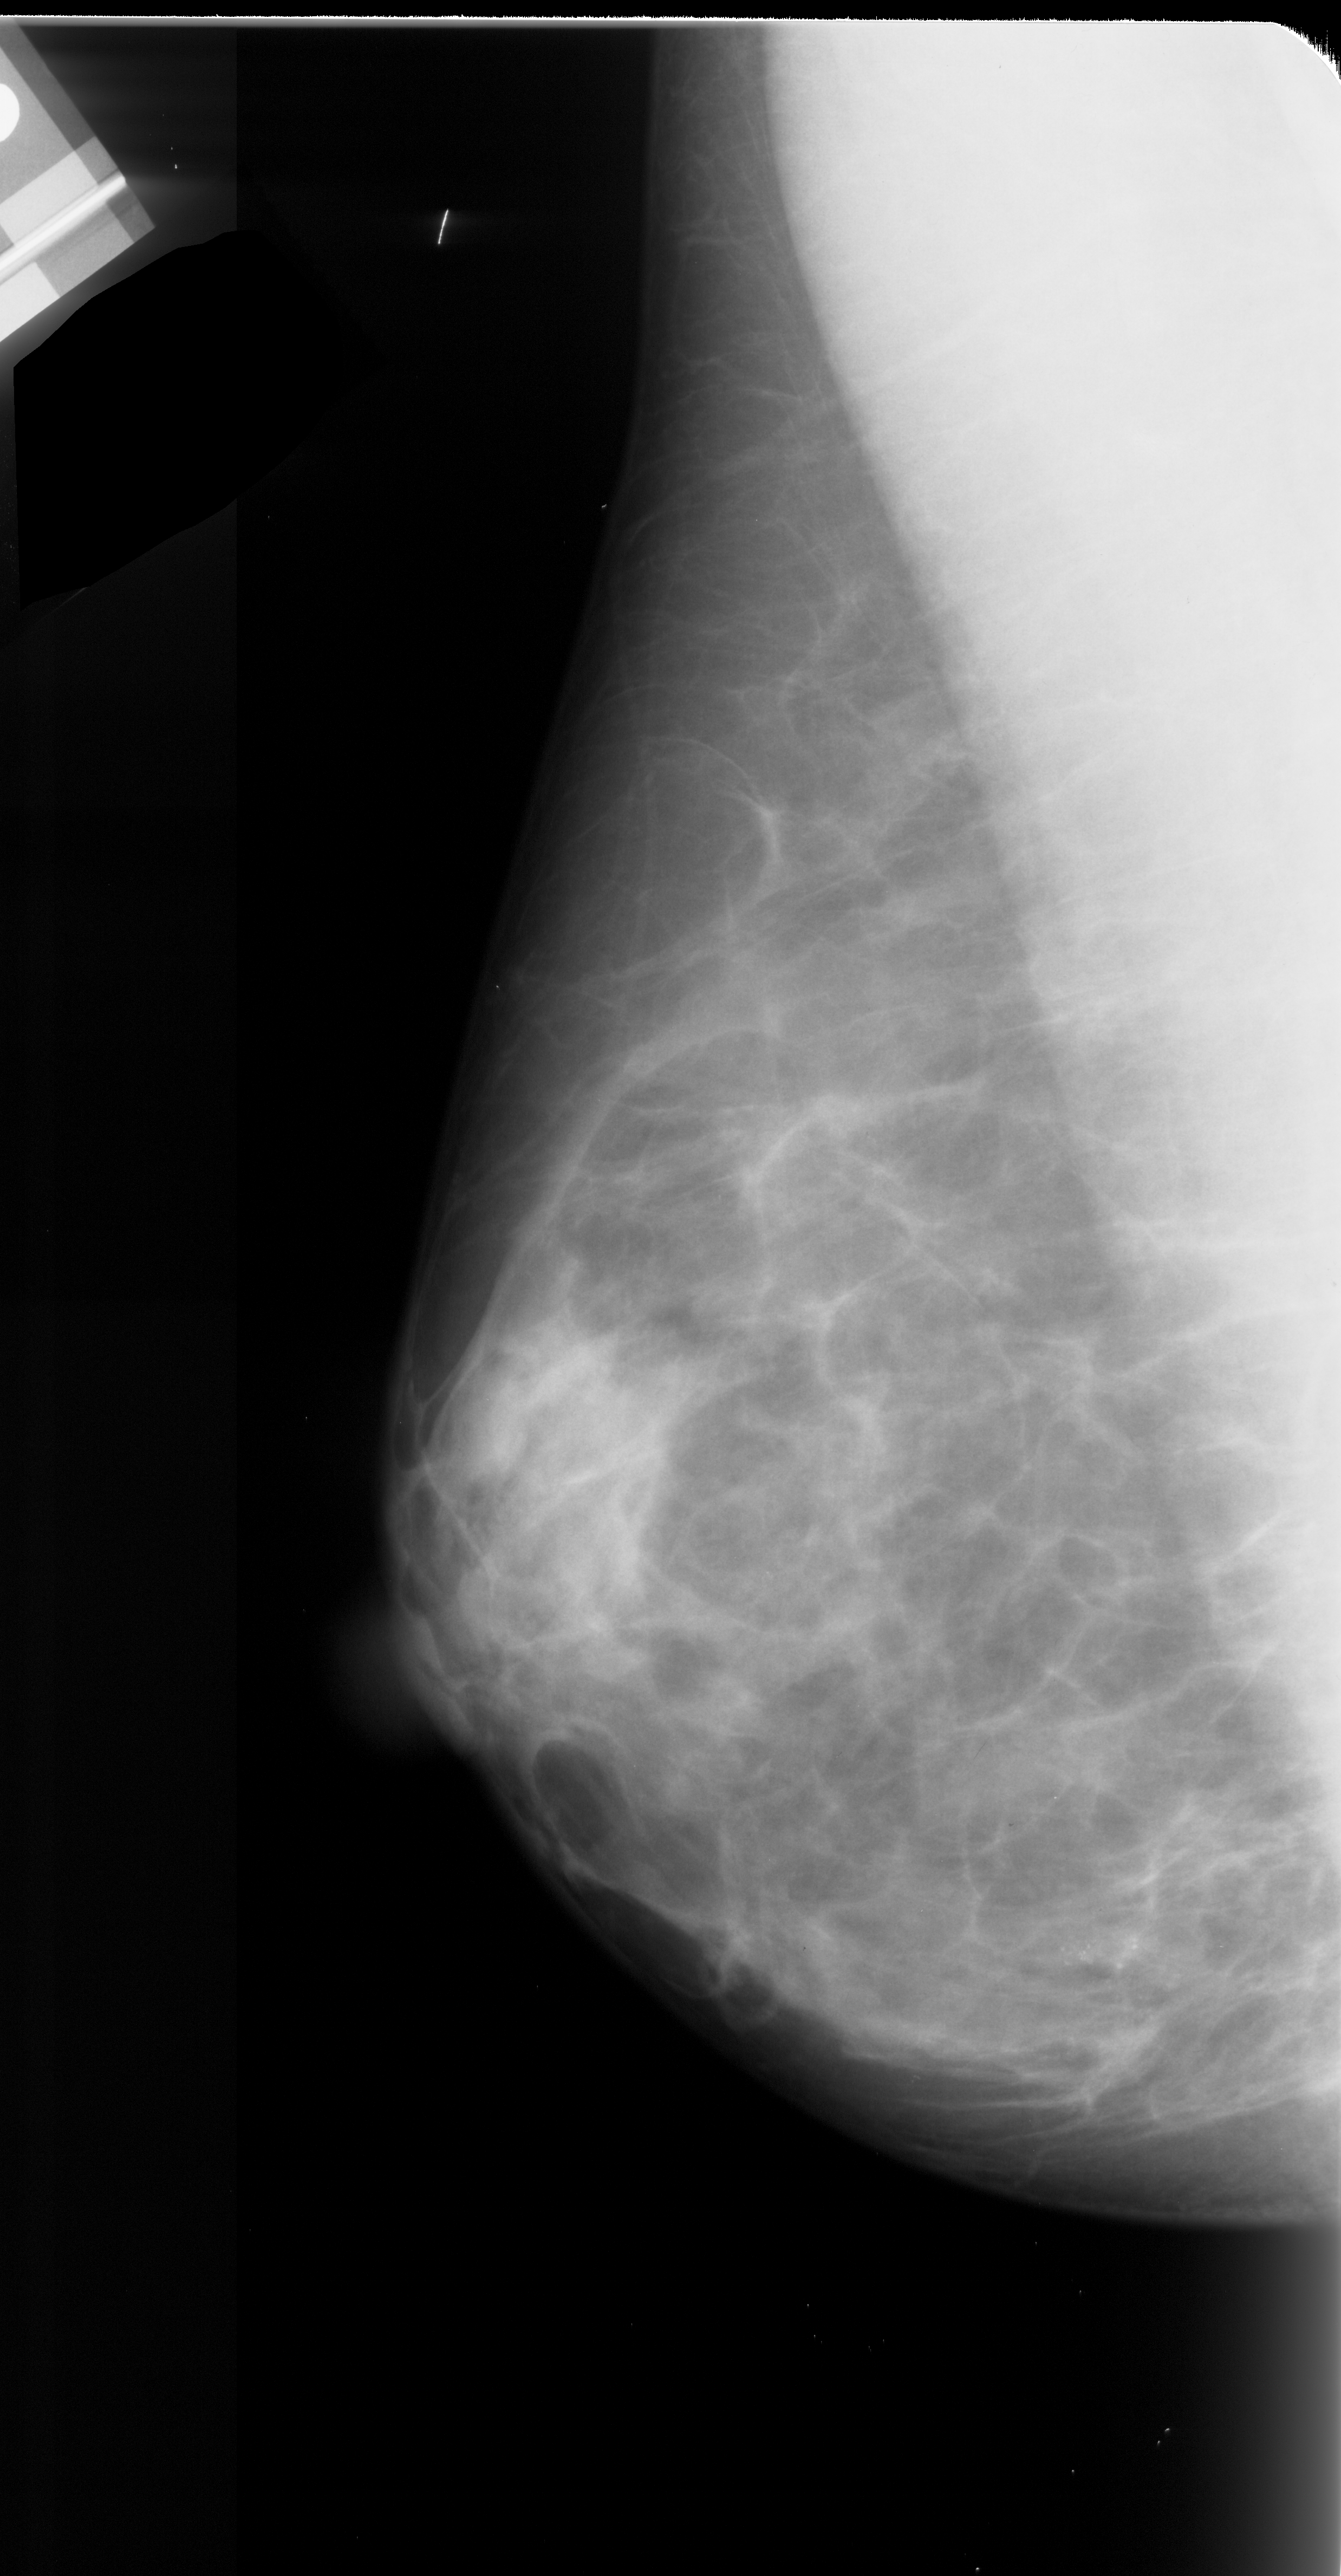
Mammogram (digitized film), left breast, mediolateral oblique (MLO) view, breast composition: almost entirely fatty (BI-RADS density category 1 of 4).
Calcifications, morphology pleomorphic, distribution clustered; BI-RADS assessment category 4; subtlety rating 3 on a 1 (subtle) to 5 (obvious) scale; pathology result (as recorded, not read from the image): malignant.